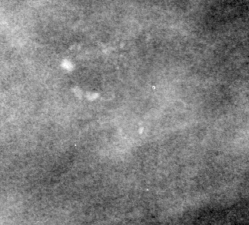
Crop from a digitized film mammogram around one marked abnormality; right breast; MLO view.
Calcifications, morphology pleomorphic, distribution clustered; BI-RADS assessment category 4; pathology result (as recorded, not read from the image): malignant.